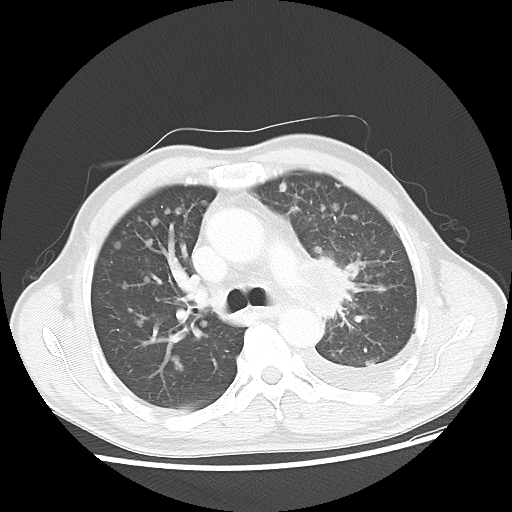
Chest CT, one axial slice. Position 30 of 47 along the scan axis. Reconstruction kernel LUNG. 100 kVp. Lung window (W 1500 / L -600 HU). 512 × 512 image matrix. Male patient, age 55 years. From the clinical record (not read from this slice): clinical TNM (as recorded): T2 N3 M1a; histopathological grade: G3.
Outlined on this slice (bounding box drawn by a radiologist):
- lung tumour (recorded histology: squamous cell carcinoma): bounding box [x1, y1, x2, y2] px = [304, 250, 381, 340]